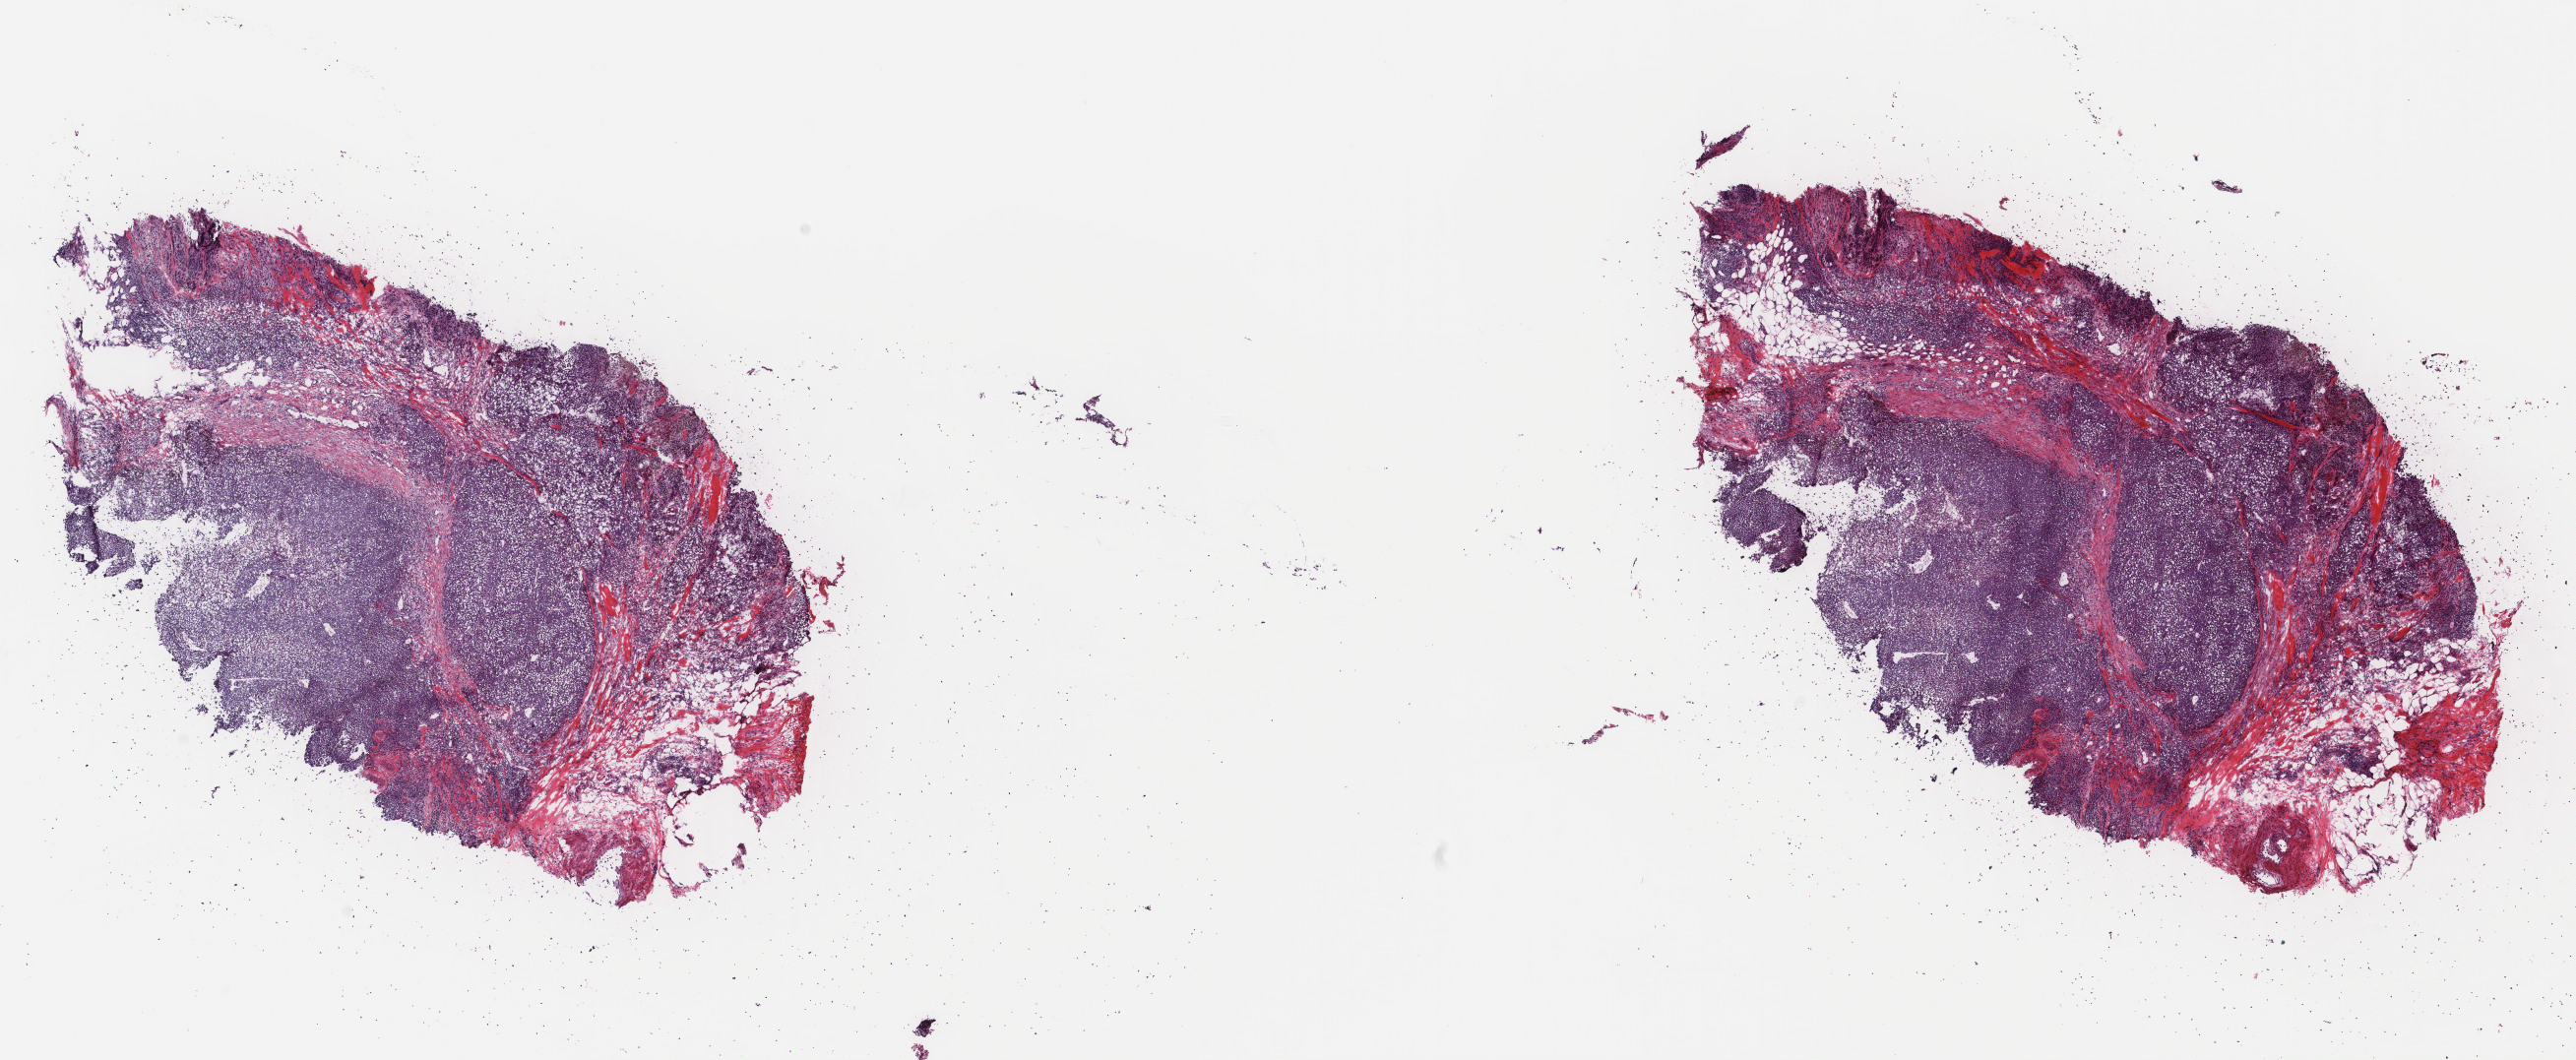
Digitized H&E tissue section (whole slide), shown as a low-resolution overview of the whole scanned area (about 20.8 x 8.6 mm); frozen section; metastatic tumour sample. Patient: male, age at initial diagnosis 67 years. Pathologist review of this section (percent, as recorded): tumour cells 75%, tumour nuclei 75%.
This section: metastatic tumour tissue. Patient diagnosis: Malignant melanoma, NOS.